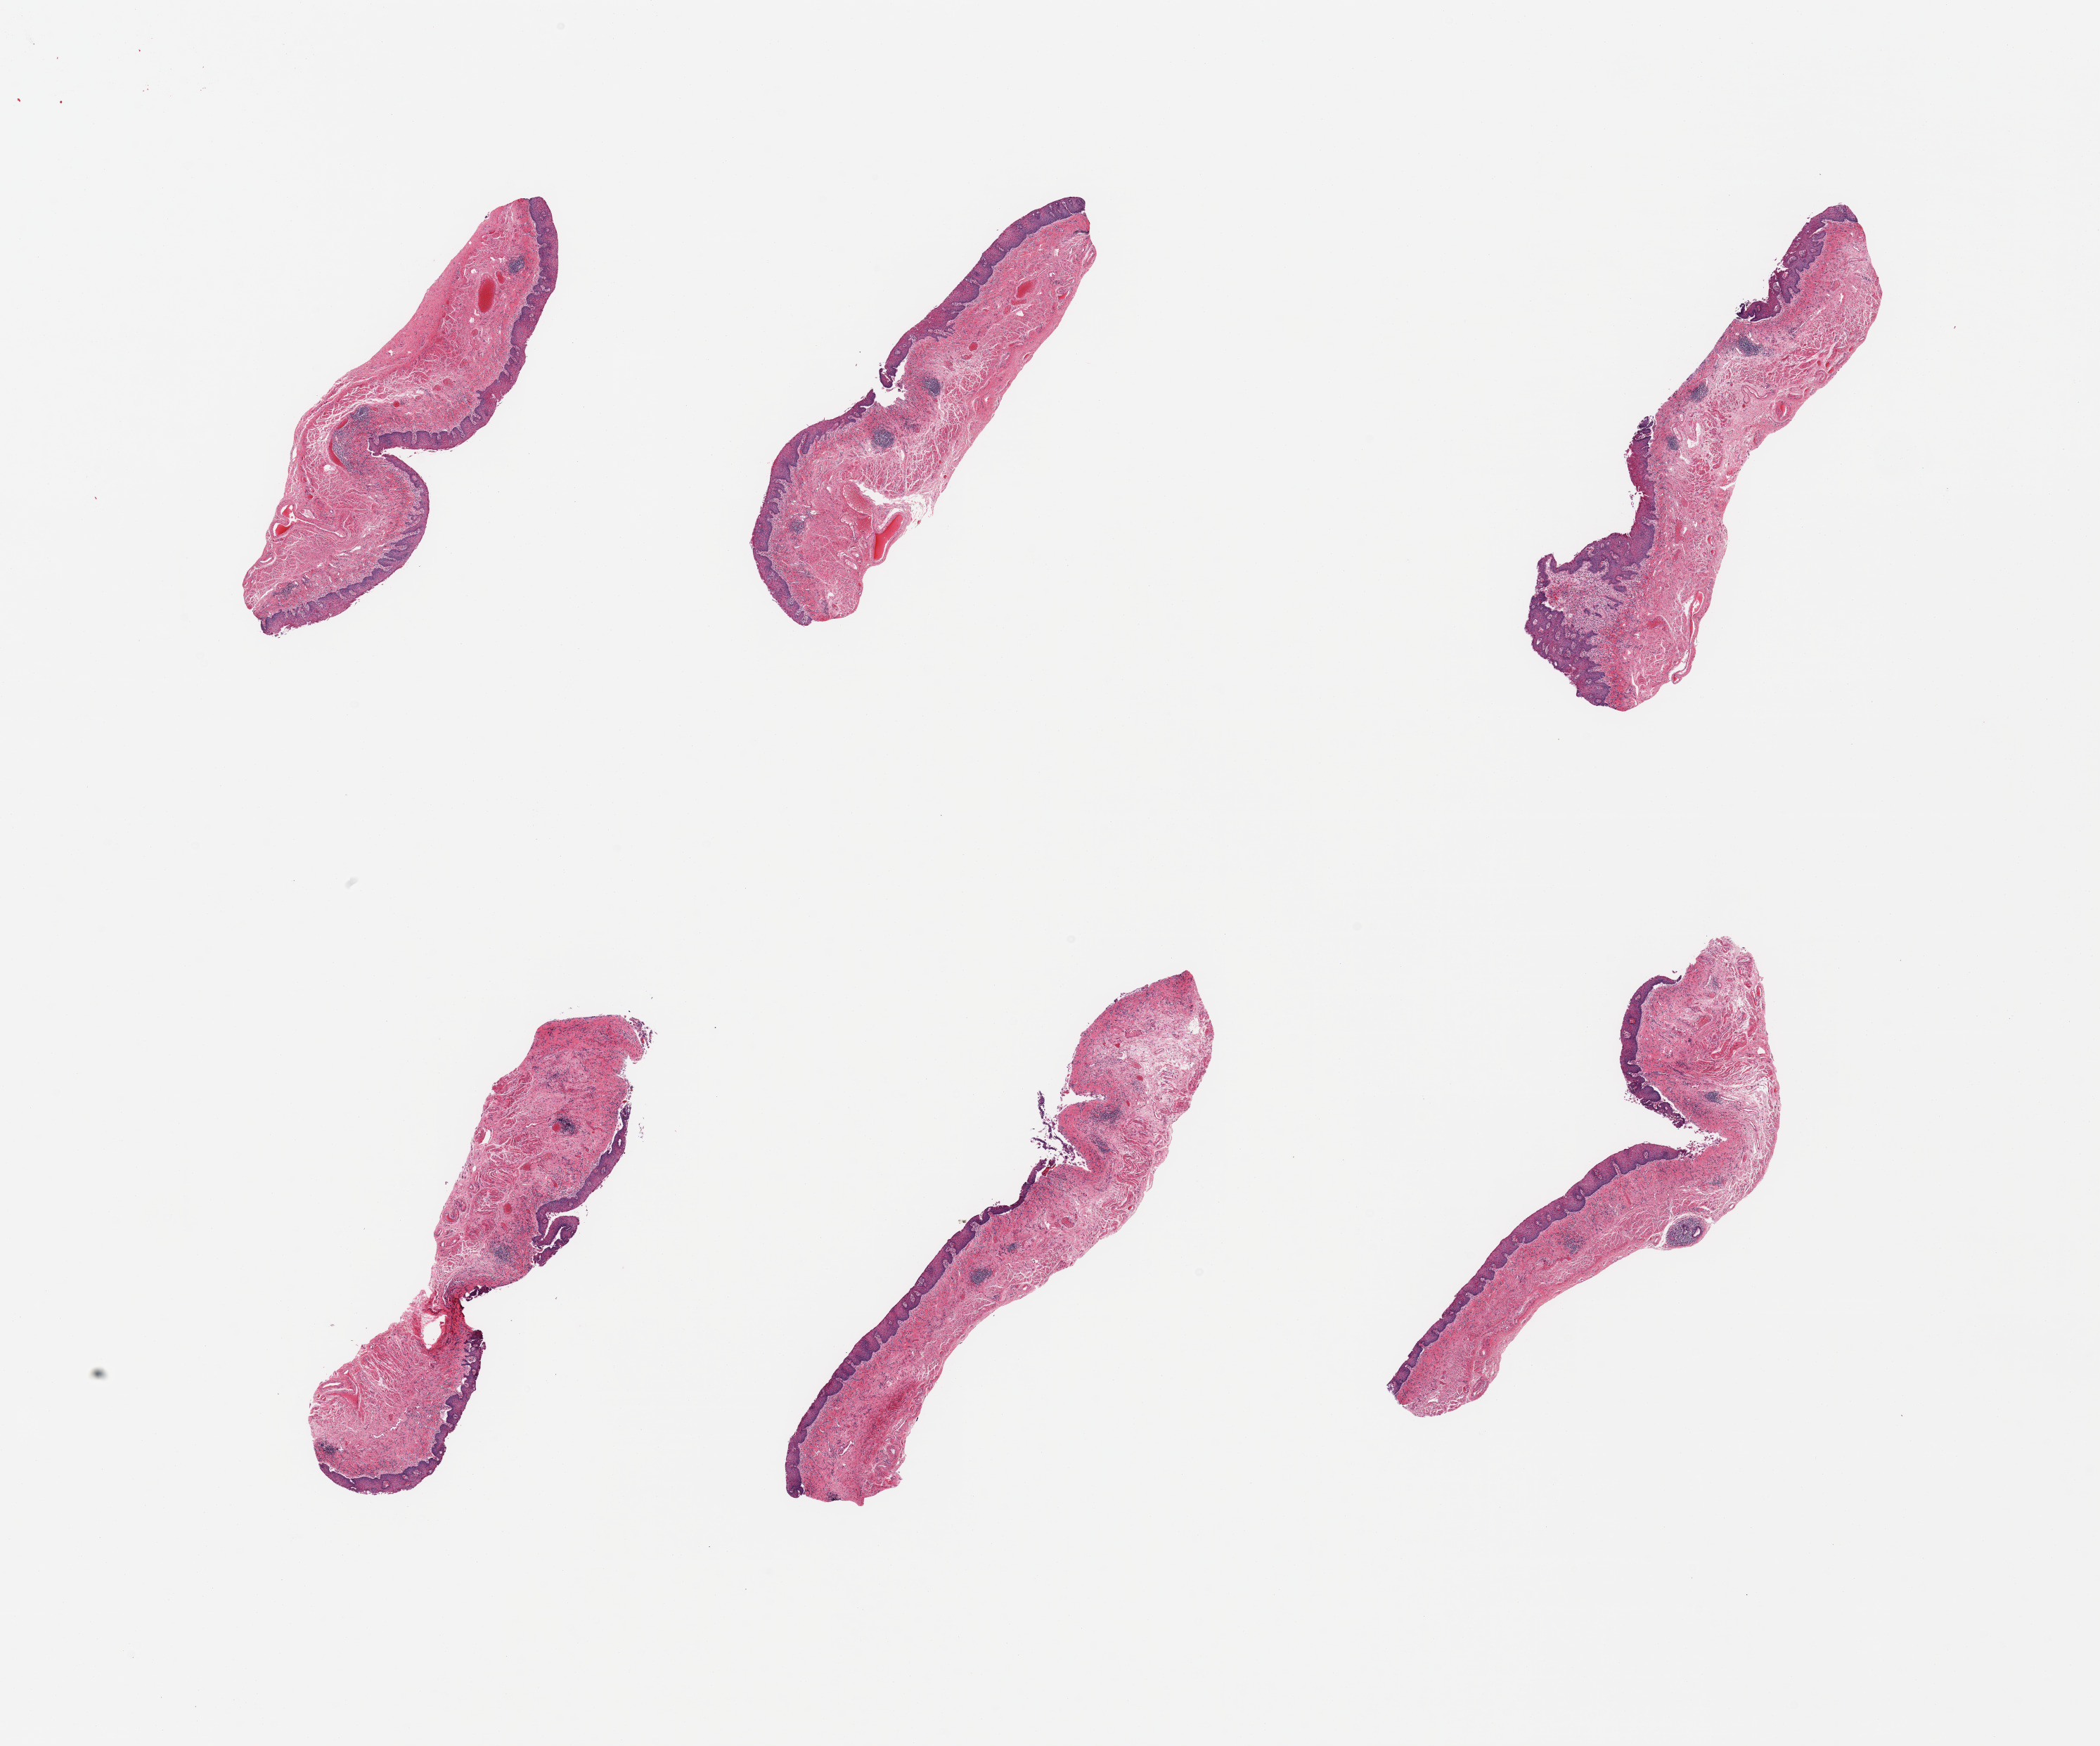
Digitized hematoxylin and eosin (H&E)-stained section — low-resolution overview of the scanned area, about 23.6 x 19.6 mm (slide scanned at 20x), PAXgene-fixed paraffin-embedded (PFPE) section, sampled site (target tissue): esophageal mucous membrane, donor tissue sample. Male donor.
Review note (as recorded): 6 pieces; foci of chronic inflammation; partial sloughing of epithelium.